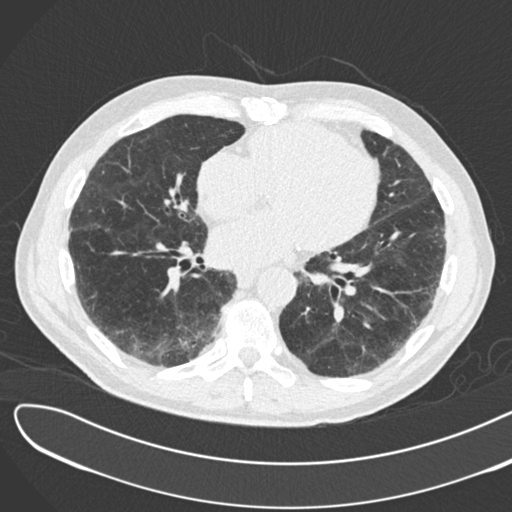
Chest CT (low-dose screening protocol), one axial image, second annual screen, lung window (W 1500 / L -600 HU), slice 109 of 183 in the series, 512 × 512 image matrix. Male, age 72 years at enrolment.
Expert-annotated lung lesion, bounding box <165,324,209,359> (left, top, right, bottom; pixels). The screening reader recorded 2 non-calcified nodules or masses ≥4 mm on this exam (right lower lobe, right lower lobe); which of them this box marks is not recorded. Participant outcome: lung cancer diagnosed 46 days after this screen — squamous cell carcinoma, NOS, right lower lobe, poorly differentiated (G3), stage IB (AJCC 6th edition), 42 mm at pathology.